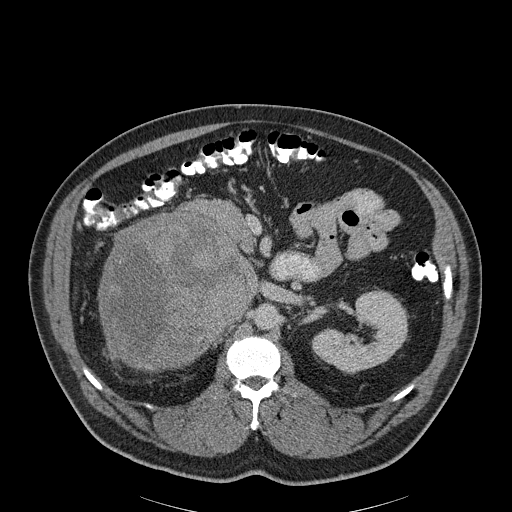
Contrast-enhanced abdominal CT, one axial slice. Position 120 of 186 along the scan axis. 120 kVp. Soft-tissue window (W 400 / L 40 HU). 3 mm slice thickness. 512 × 512 image matrix, field of view 464 × 464 mm. Patient: male, 56 years. From the clinical record (not read from this slice): diagnosis: adrenocortical carcinoma; tumour side: right adrenal; tumour size at pathology: 18 cm; Ki-67 index: 2 %; stage (as recorded): 3.
Annotated regions visible in this slice (semi-automatic segmentation, software-assisted and operator-edited):
- mass: box from (x=101, y=216) to (x=246, y=364) px